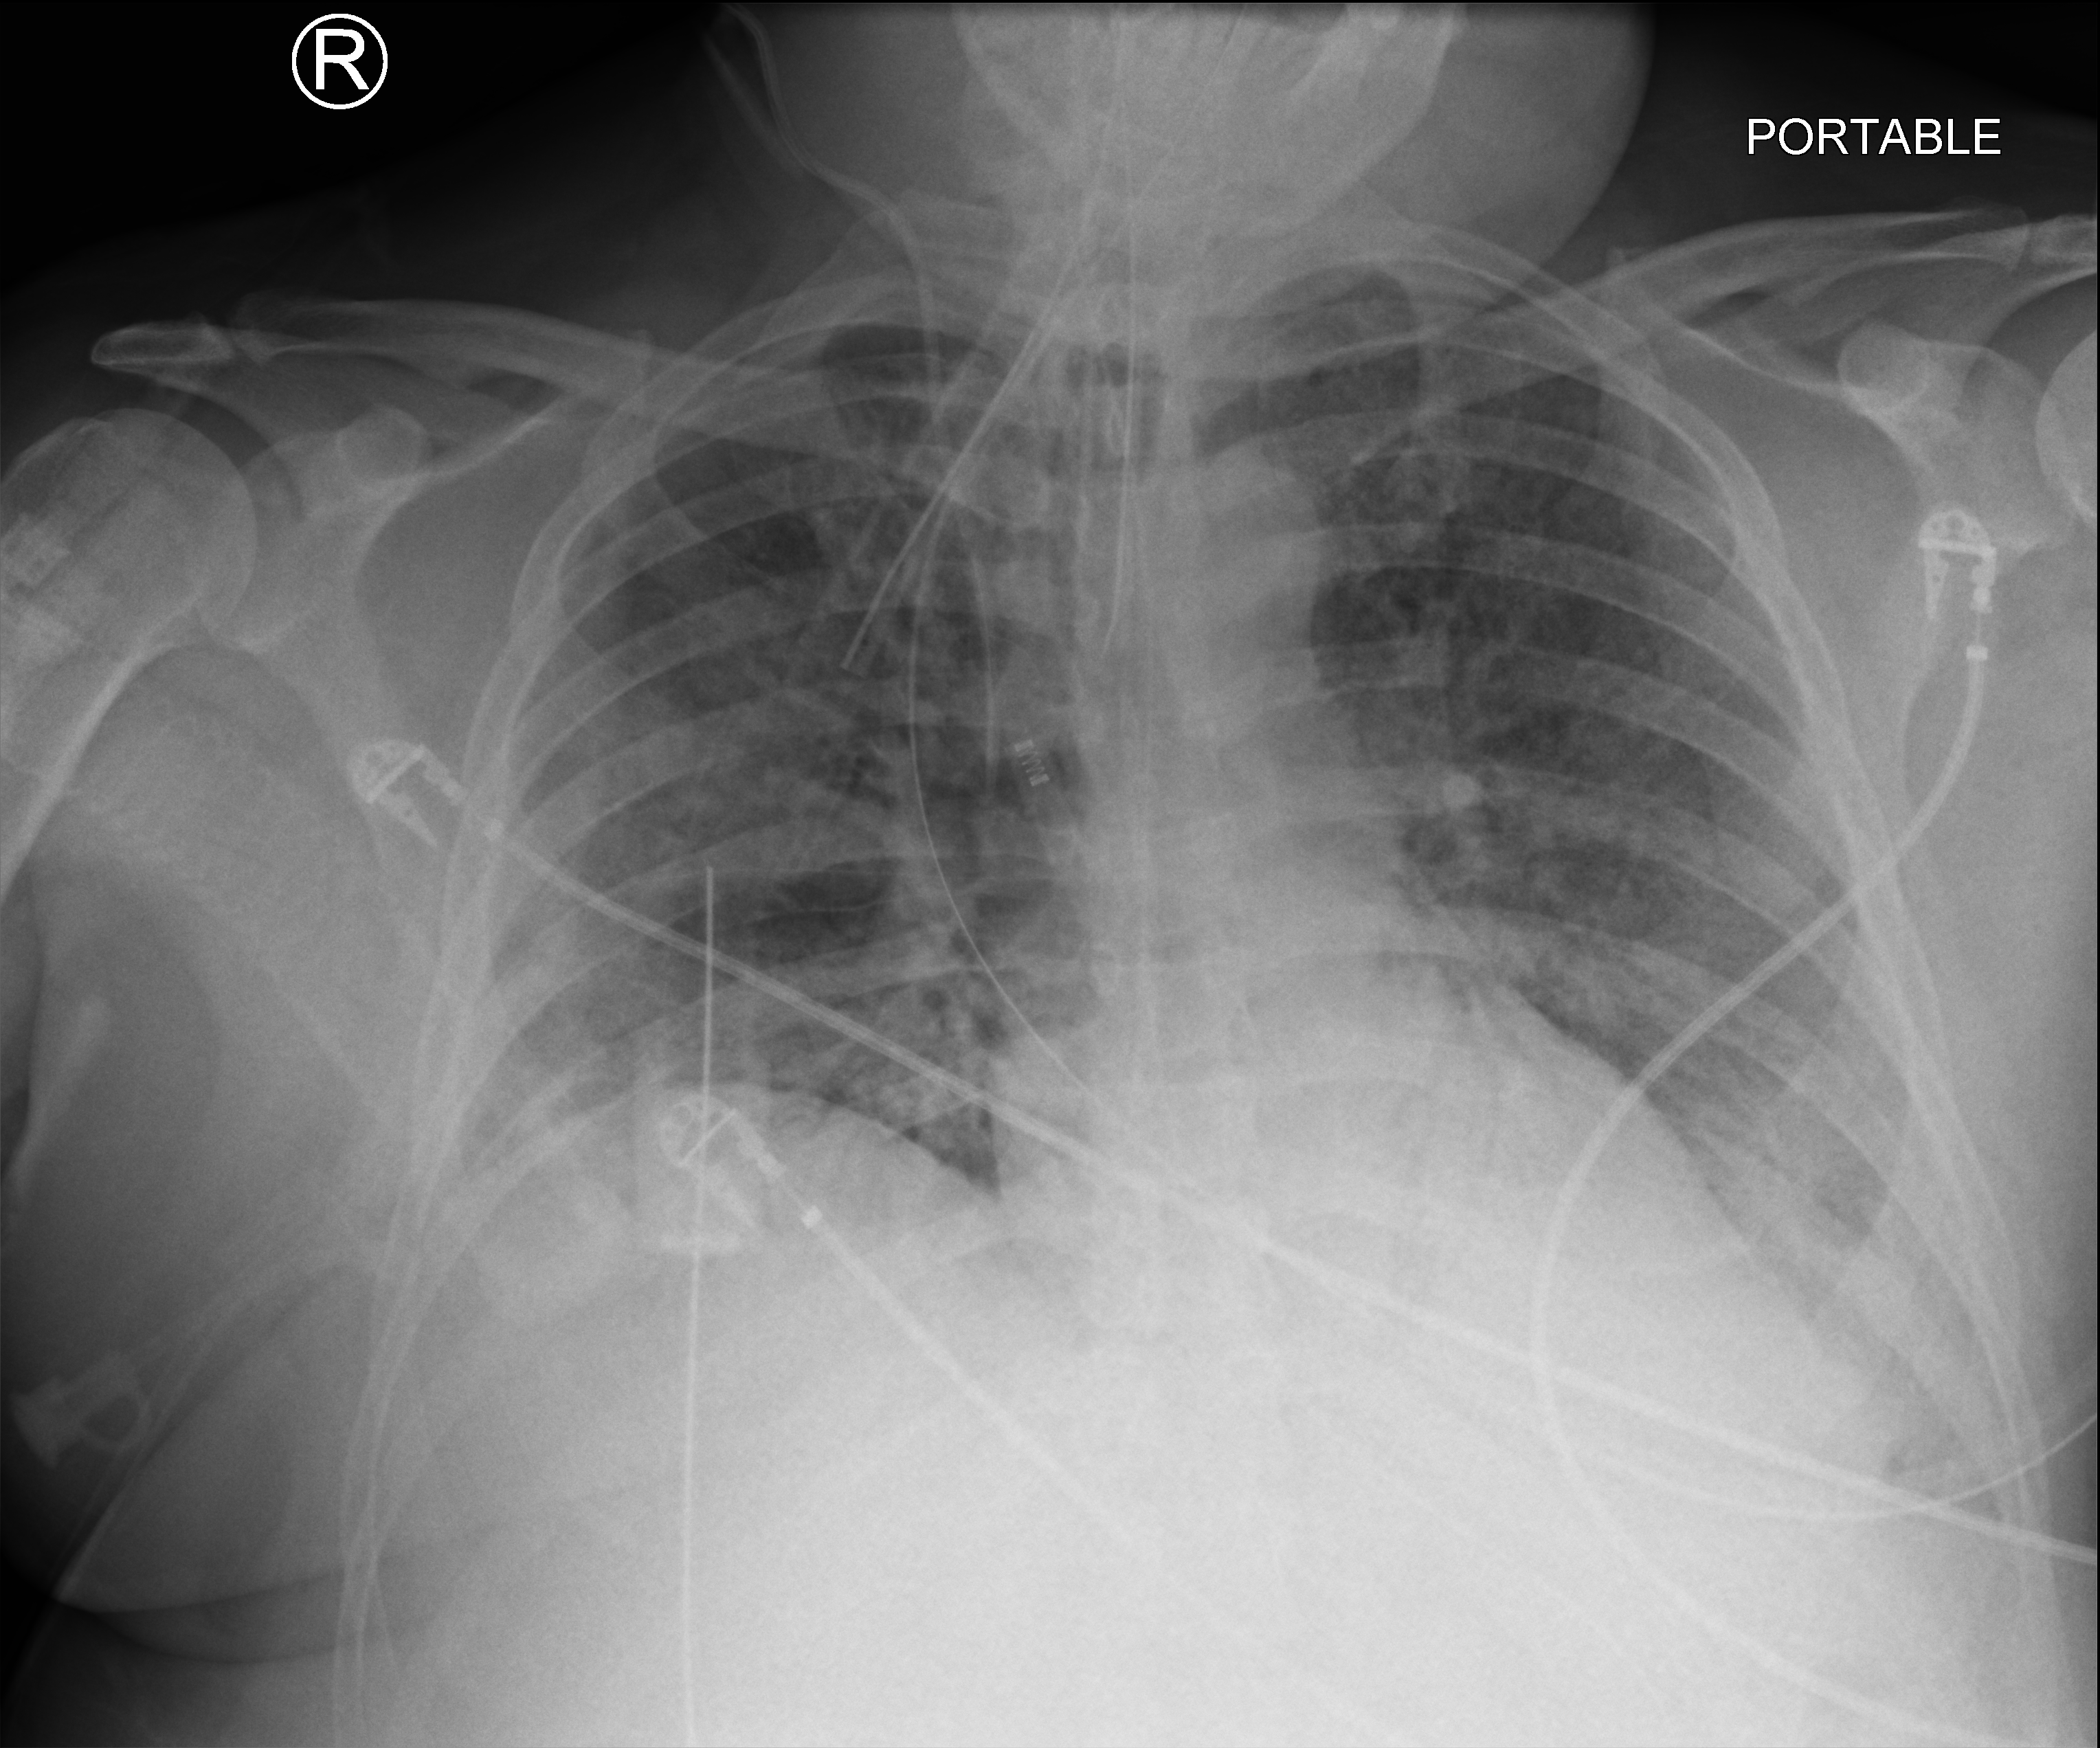
Chest X-ray (portable). Male patient hospitalised with COVID-19, age 18–59 years.
Hospital-stay facts (about this admission, not read from this image; timing relative to this image not recorded):
- admitted to intensive care during this hospital stay: yes
- other chronic lung disease (admission record): no